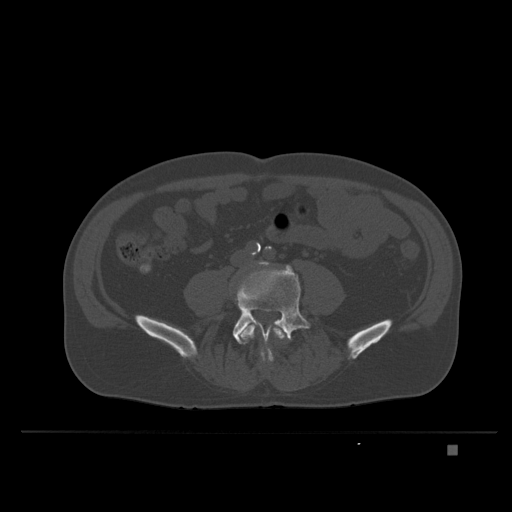
CT including the spine, one axial slice; slice 63 of 435 in the series (ordered by position); bone window (W 1800 / L 400 HU); 1.5 mm slice thickness; 512 × 512 image matrix. Male patient, age 73 years. Case-level facts recorded for this patient, not image findings: primary cancer: skin.
Outlined on this slice (semi-automatic segmentation, software-assisted and operator-edited):
- L4 vertebra: box from (x=238, y=318) to (x=286, y=369) px
- L5 vertebra: (x=233, y=267)–(x=310, y=344)